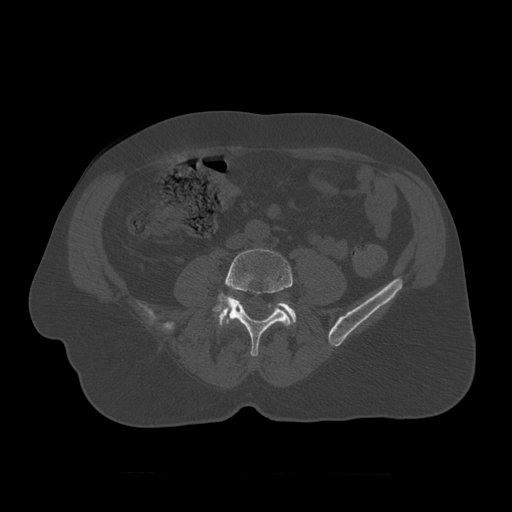
CT including the spine, one axial slice; slice 274 of 450 in the series (ordered by position); 120 kVp; bone window (W 1800 / L 400 HU); 512 × 512 image matrix, field of view 405 × 405 mm. Patient age 75 years. From the clinical record (not read from this slice): primary cancer: prostate.
Annotated regions visible in this slice (semi-automatic segmentation, software-assisted and operator-edited):
- L4 vertebra: bounding box [x1, y1, x2, y2] px = [212, 249, 293, 357]
- L5 vertebra: [214, 301, 297, 329]